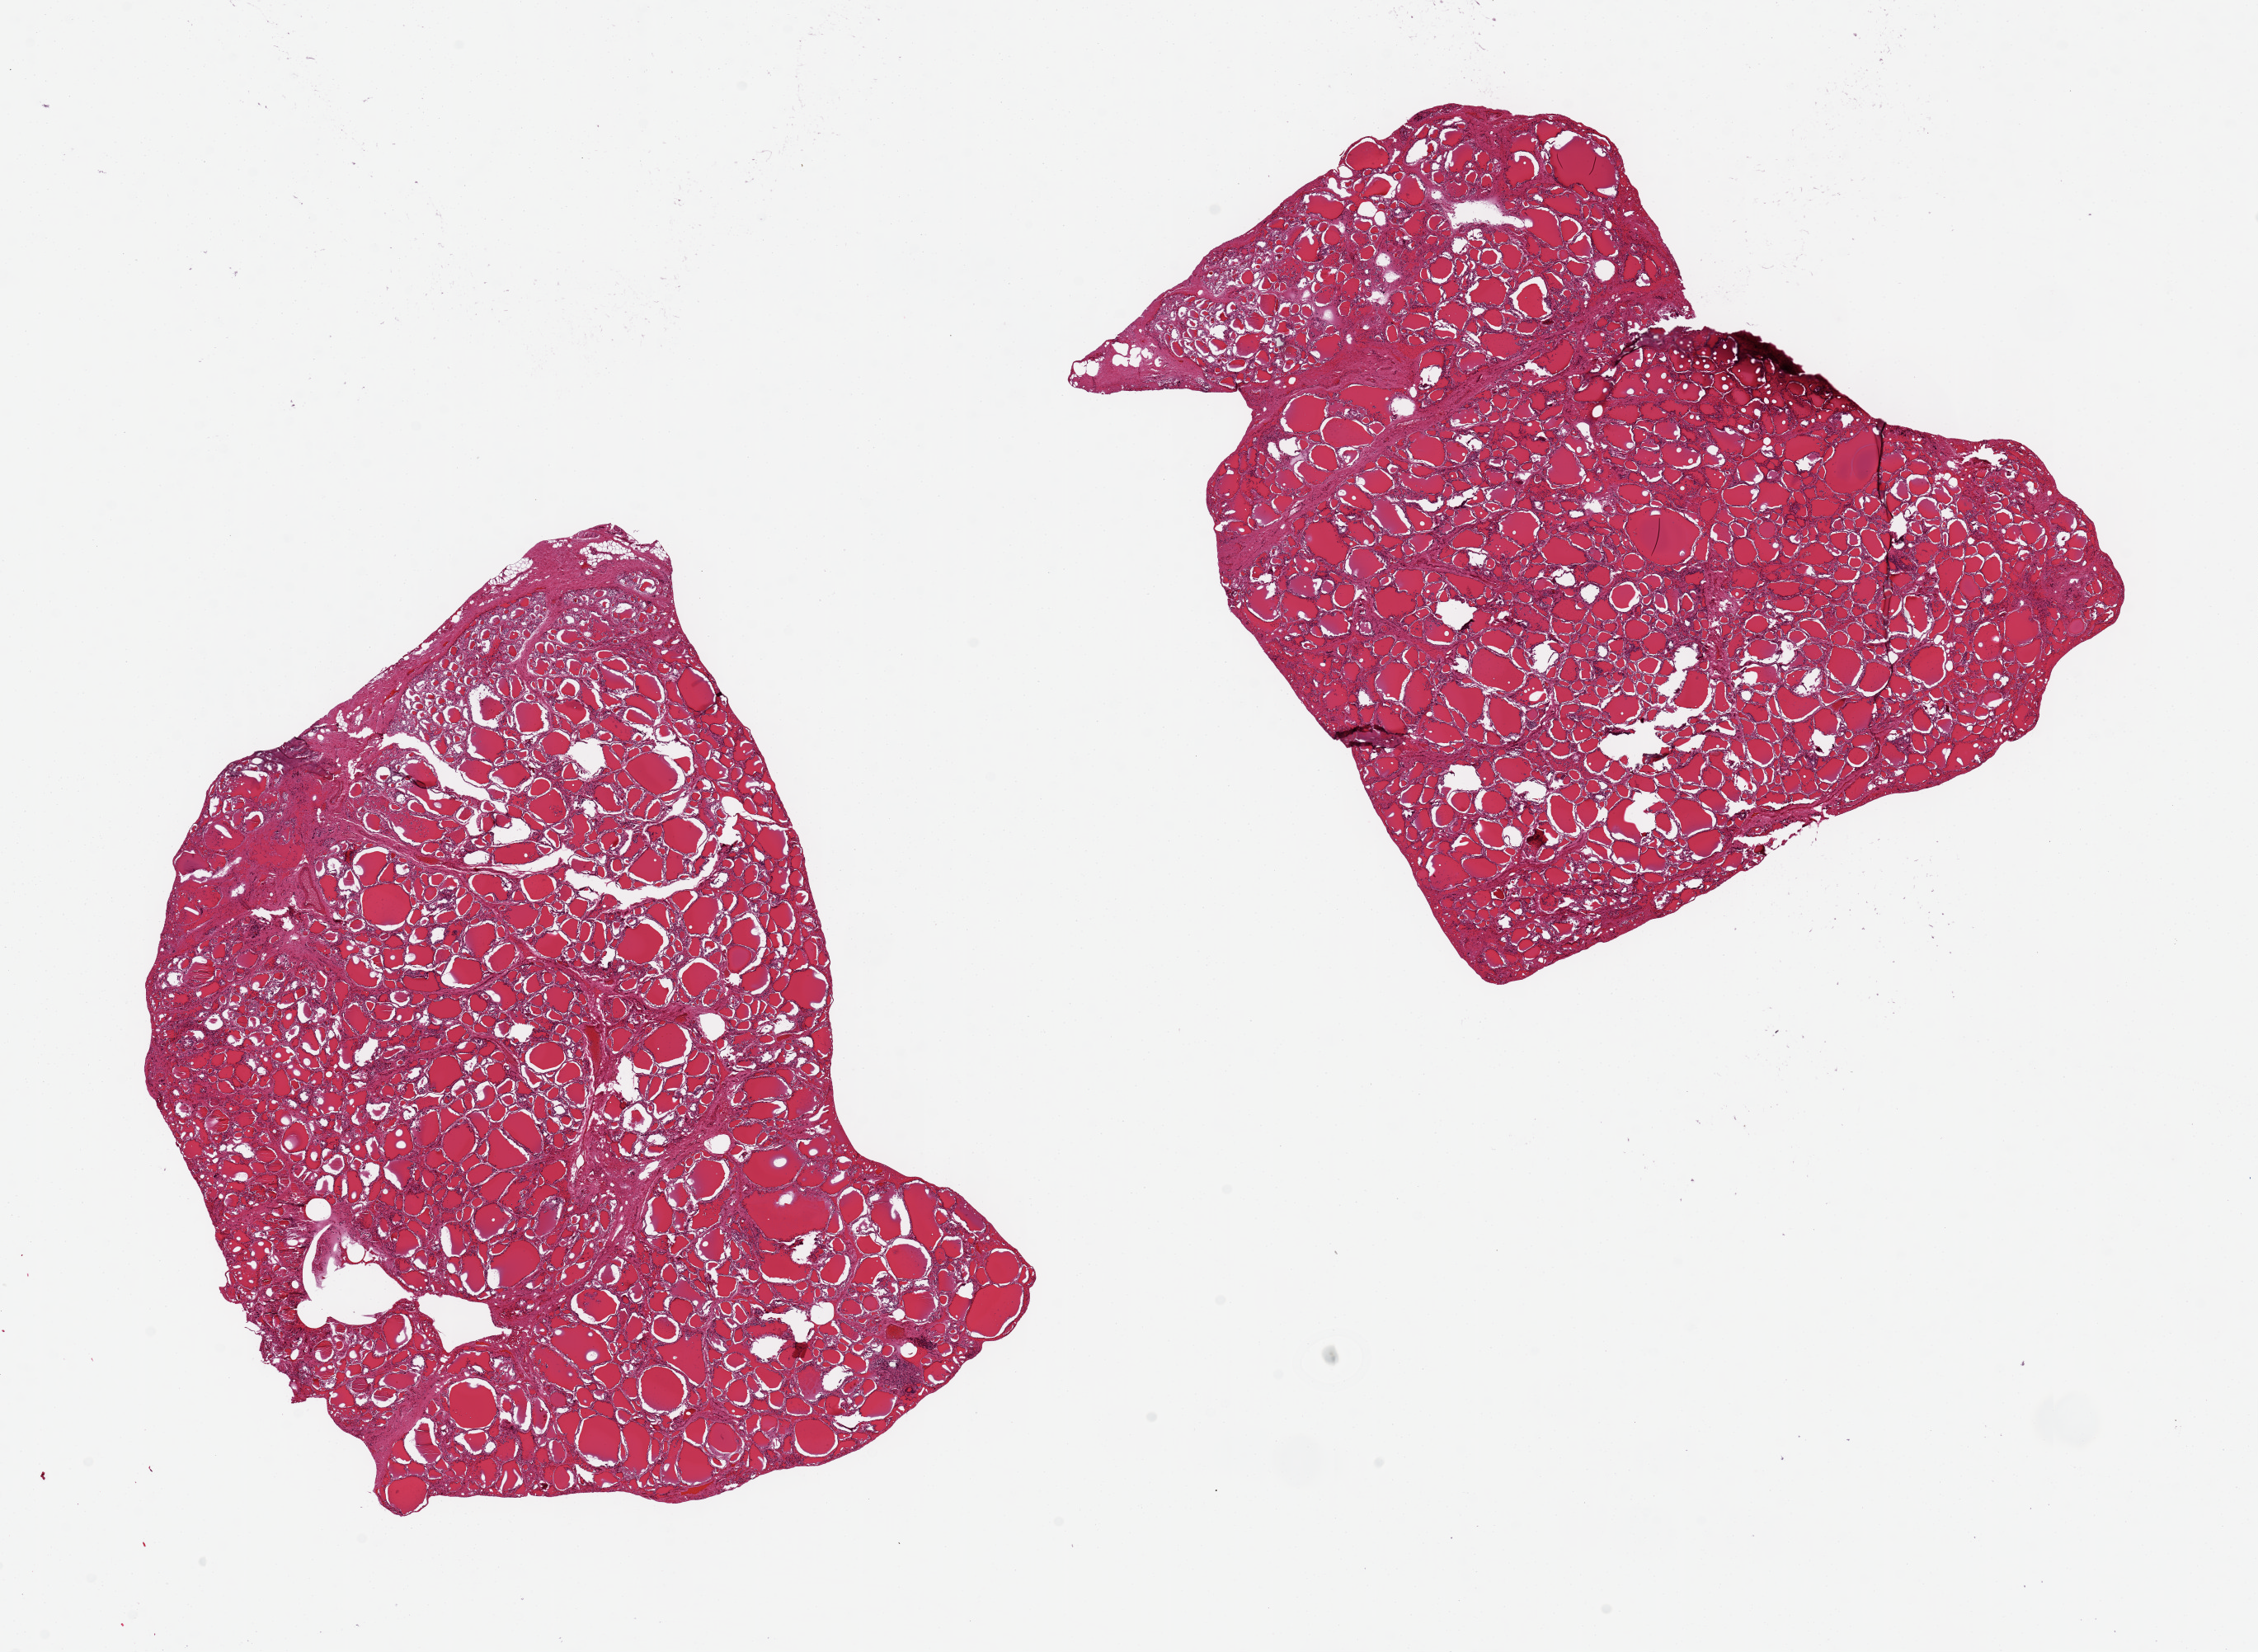
Whole-slide image, haematoxylin and eosin stain — a low-resolution overview of the entire scanned area, about 21.7 x 15.8 mm (acquisition: 20x scan). PAXgene-fixed paraffin-embedded (PFPE) section. Target tissue: thyroid. Donor tissue sample. Male donor.
* review note (as recorded): 2 pieces, 8.7x6 & 7x7 mm